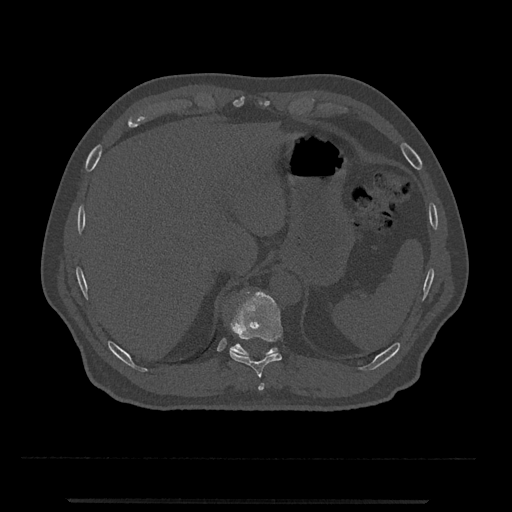
CT including the spine, one axial slice; position 503 of 797 along the scan axis; reconstruction kernel Br40s/3; 120 kVp; bone window (W 1800 / L 400 HU); 0.5 mm slice thickness; 512 × 512 image matrix. Male patient, age 63 years. From the clinical record (not read from this slice): primary cancer: prostate.
Outlined on this slice (semi-automatically segmented with operator editing):
- T10 vertebra: bounding box <230,291,283,379> (left, top, right, bottom; pixels)
- T11 vertebra: <230,343,278,356>
- T9 vertebra: <258,383,265,391>